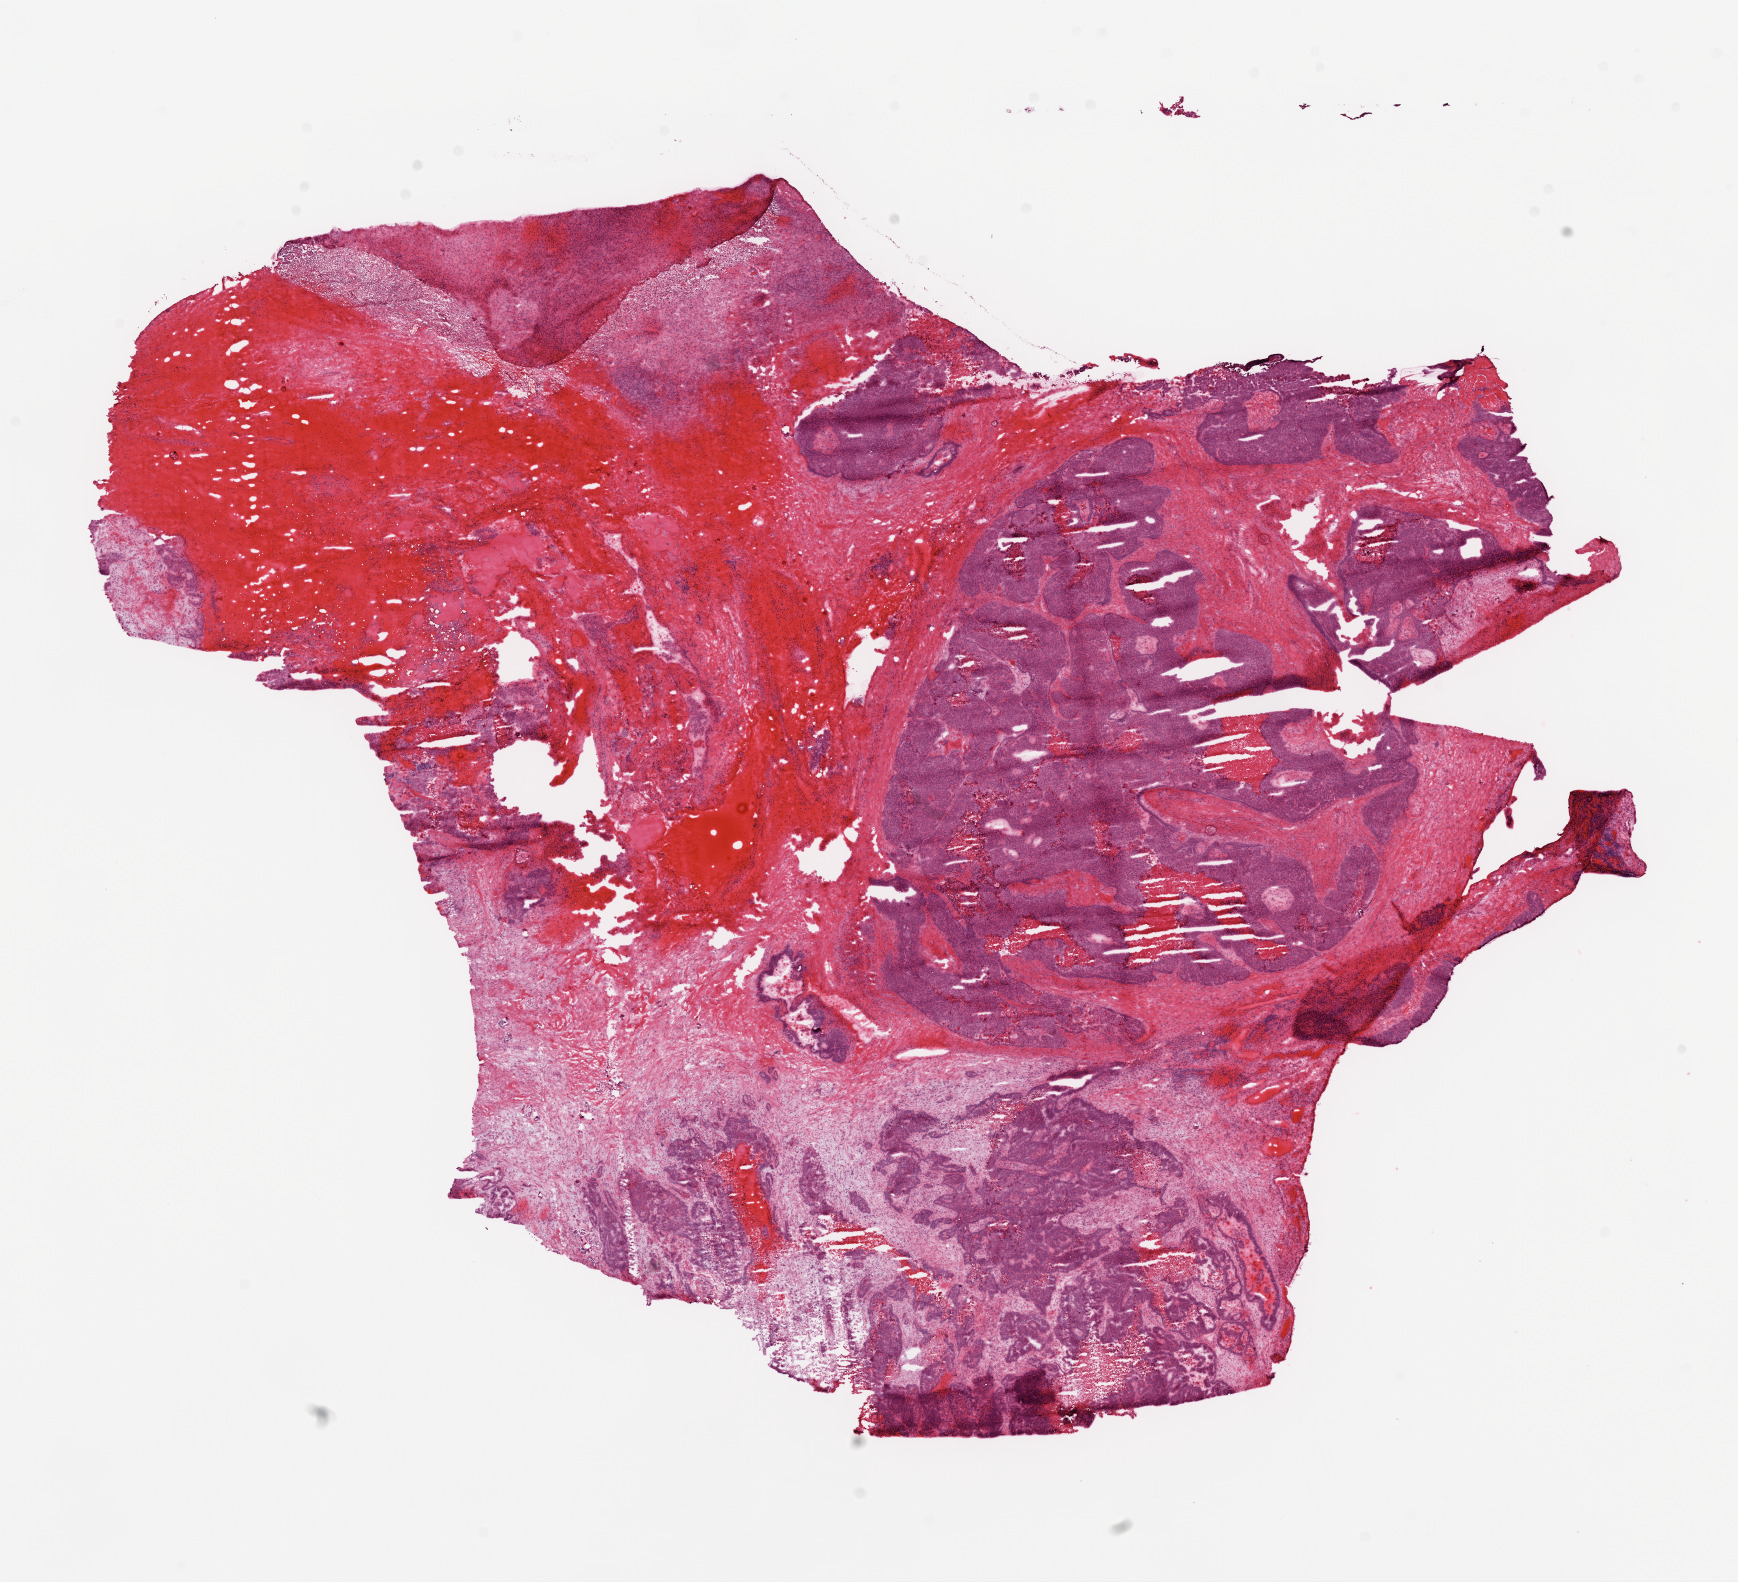
H&E whole-slide image — shown as a low-resolution overview of the whole scanned area (about 14.0 x 12.8 mm, from a 20x scan), frozen section from the top of the tissue portion, ovary, primary tumour sample. Female patient; age at initial diagnosis 66 years. Histologic grade: G3 (poorly differentiated). Pathologist review of this section (percent, as recorded): tumour cells 50%, tumour nuclei 85%, normal cells 0%, stromal cells 40%, necrosis 10%.
Diagnosis: Serous cystadenocarcinoma, NOS. FIGO stage: IIIC. Laterality: bilateral.